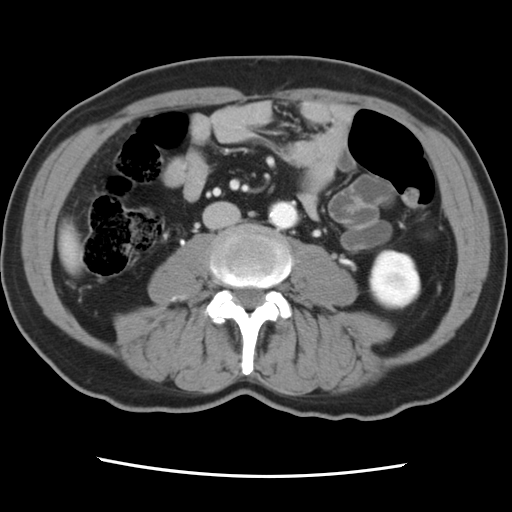
Contrast-enhanced abdominal CT, one axial slice. Position 13 of 83 along the scan axis. 120 kVp. Intravenous contrast given. Soft-tissue window (W 400 / L 40 HU). 512 × 512 image matrix, field of view 321 × 321 mm. Male patient, age 69 years. Case-level facts recorded for this patient, not image findings: diagnosis: colorectal cancer liver metastases, imaged before liver resection; multiple liver metastases: yes.
Outlined on this slice (expert manual segmentation):
- liver: bounding box <62,232,80,269> (left, top, right, bottom; pixels)
- planned liver remnant (the part of the liver to remain after resection): <61,231,80,269>